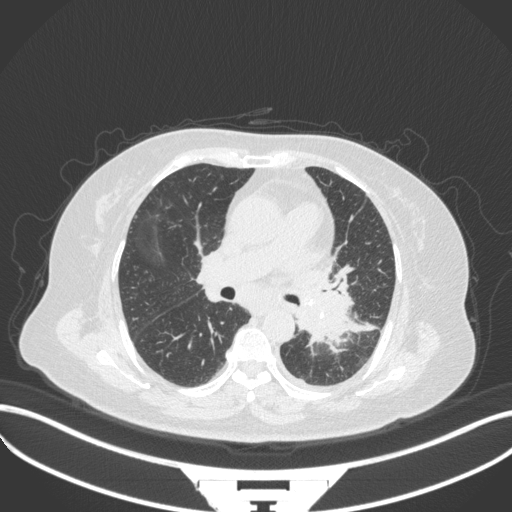
Chest CT, one axial slice. Position 195 of 328 along the scan axis. Reconstruction kernel B31f. 120 kVp. Lung window (W 1500 / L -600 HU). 1 mm slice thickness. 512 × 512 image matrix, field of view 400 × 400 mm. Patient: female, 69 years. Case-level facts recorded for this patient, not image findings: clinical TNM (as recorded): T2b N3 M1.
Annotated regions visible in this slice (bounding box drawn by a radiologist):
- lung tumour (recorded histology: adenocarcinoma): bounding box [x1, y1, x2, y2] px = [291, 277, 358, 353]